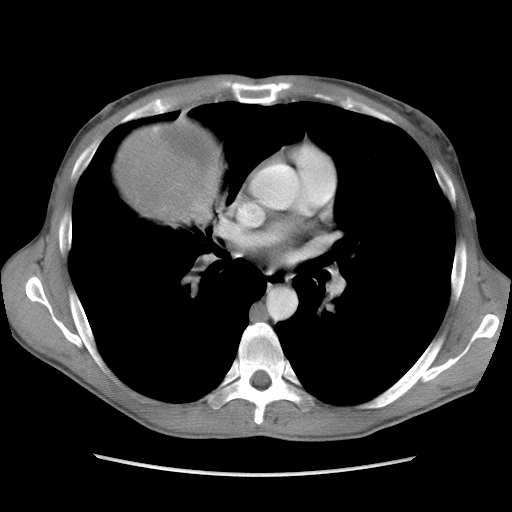
Contrast-enhanced abdominal CT, one axial slice; position 105 of 115 along the scan axis; soft-tissue window (W 400 / L 40 HU); 512 × 512 image matrix, field of view 360 × 360 mm. Male patient. Case-level facts recorded for this patient, not image findings: diagnosis: adrenocortical carcinoma; tumour side: right adrenal; Ki-67 index: 13 %; stage (as recorded): 3.
Outlined on this slice (semi-automatically segmented with operator editing):
- mass: bounding box (x1, y1, x2, y2) in pixels: (122, 118, 224, 221)